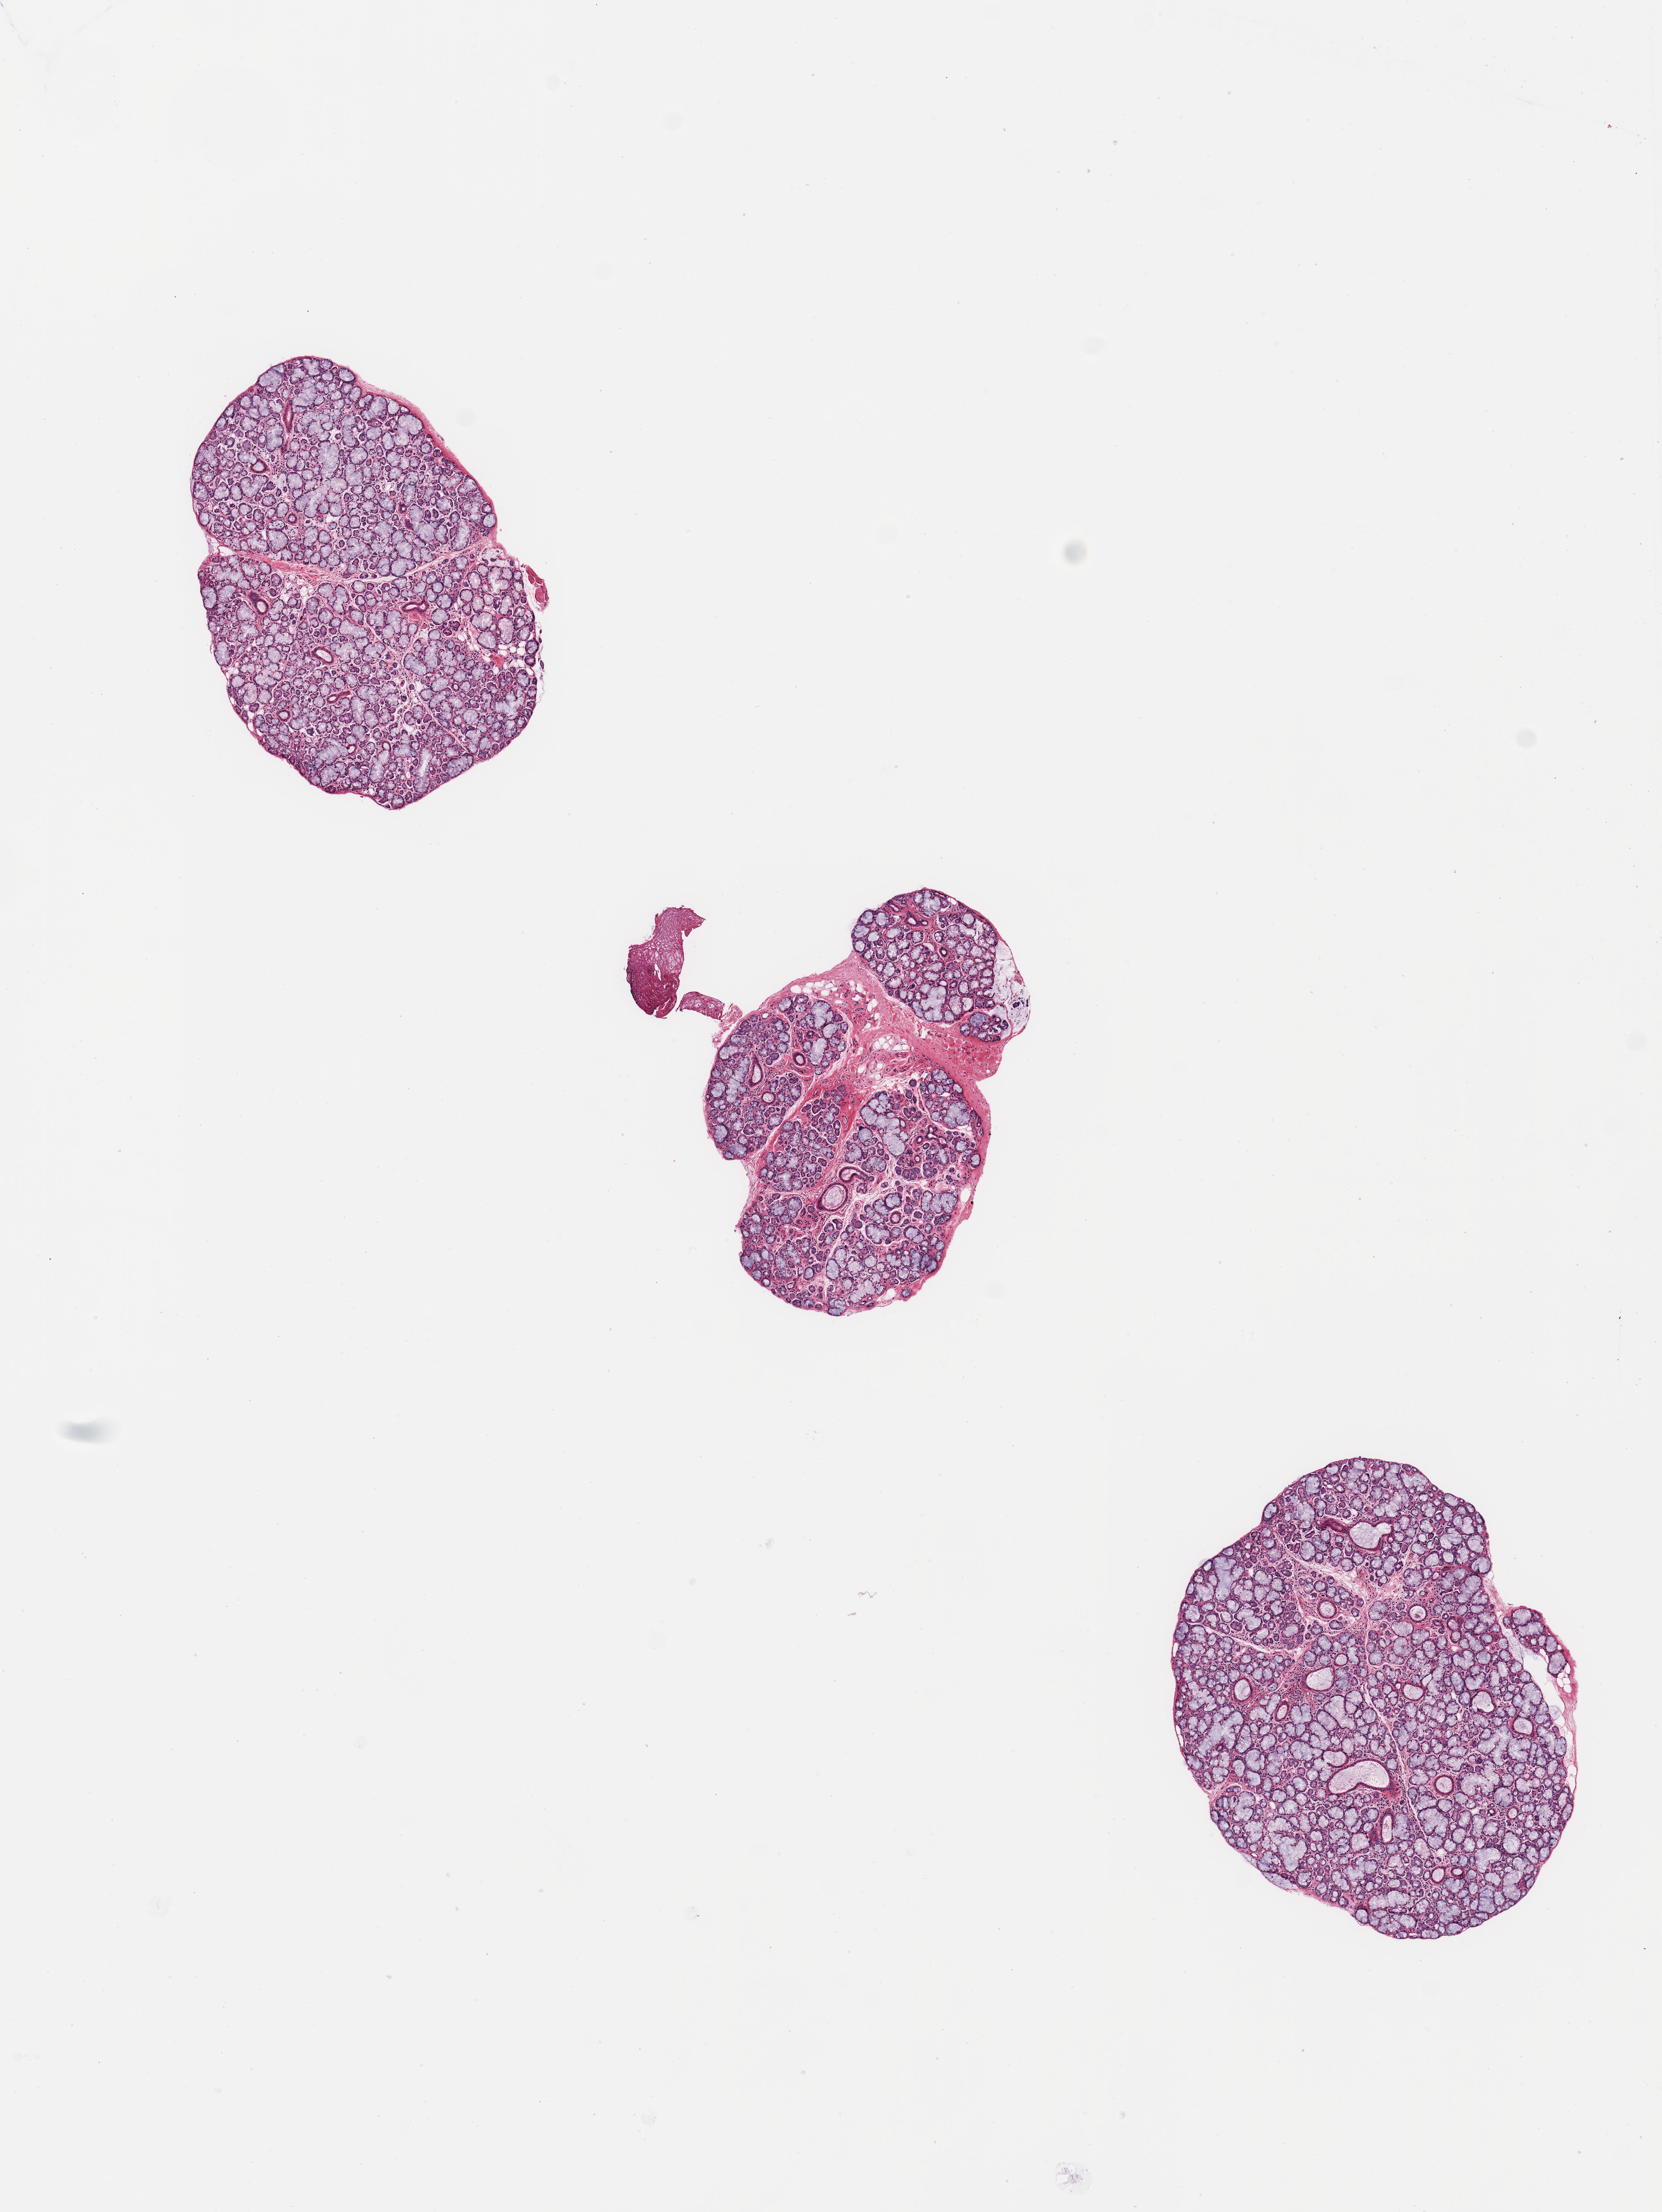
Hematoxylin and eosin (H&E) whole-slide image, low-resolution overview of the scanned area, about 8.9 x 11.8 mm; PAXgene-fixed, paraffin-embedded tissue; target tissue: minor salivary gland; tissue donor sample.
Review note (as recorded): 3 pieces; ~90% glandular parenchymal & ductal elements, good specimen.